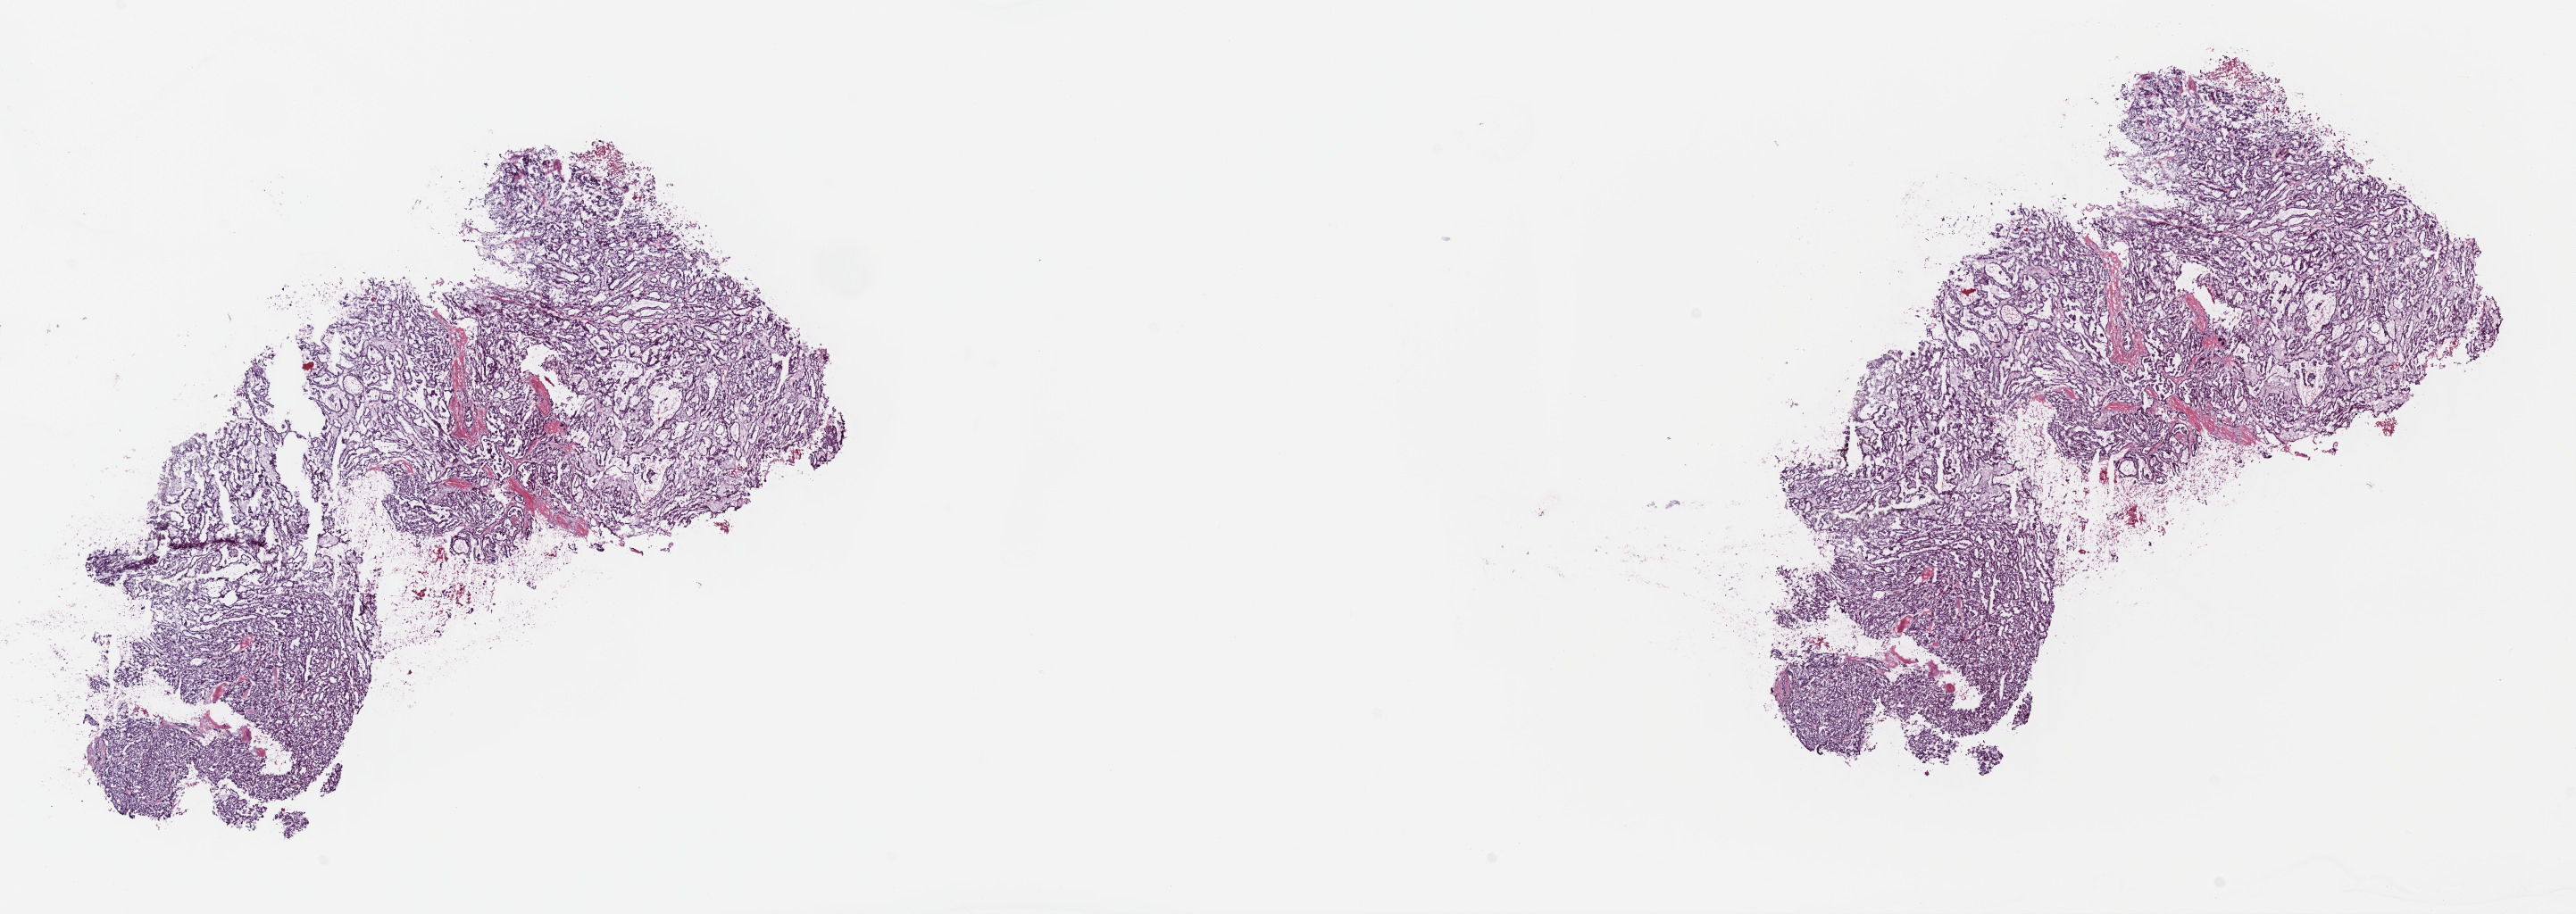
Digitized H&E-stained tissue section (whole slide) — whole scanned area (about 22.7 x 8.0 mm, slide scanned at 40x) shown as a low-resolution overview, frozen section from the top of the tissue portion, primary tumour sample from the kidney. Male patient; age at initial diagnosis 66 years. Pathologist review of this section (percent, as recorded): tumour cells 80%, tumour nuclei 80%, normal cells 0%, stromal cells 20%, necrosis 0%. Inflammatory infiltration, as recorded: lymphocyte infiltration 0%, monocyte infiltration 5%, neutrophil infiltration 0%.
Diagnosis: Papillary adenocarcinoma, NOS. AJCC pathologic stage: I.